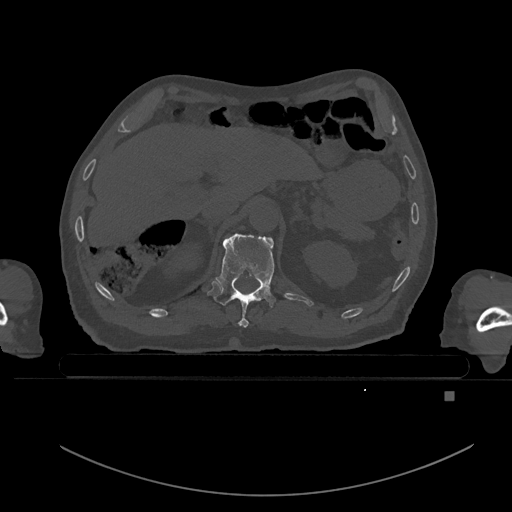
CT including the spine, one axial slice; position 28 of 969 along the scan axis; bone window (W 1800 / L 400 HU); 0.5 mm slice thickness; 512 × 512 image matrix, field of view 456 × 456 mm. Patient: male, 82 years. From the clinical record (not read from this slice): primary cancer: prostate; vertebrae with lytic lesions (as recorded): T11, T9, T8, T2.
Structures marked on this image (semi-automatically segmented with operator editing):
- T11 vertebra: bounding box <214,233,277,327> (left, top, right, bottom; pixels)